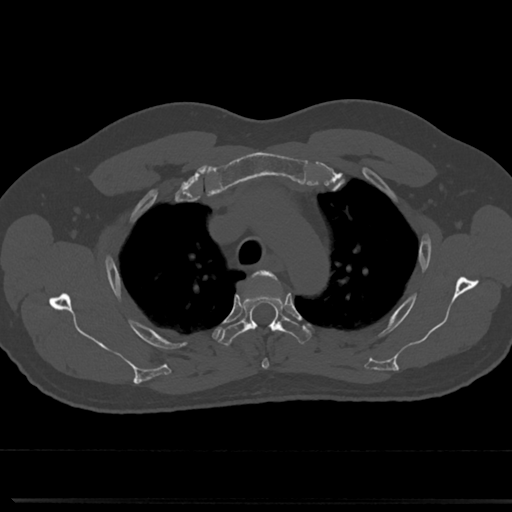
CT including the spine, one axial slice; position 561 of 817 along the scan axis; 120 kVp; bone window (W 1800 / L 400 HU); 512 × 512 image matrix. Male patient, age 61 years. From the clinical record (not read from this slice): primary cancer: prostate.
Structures marked on this image (semi-automatic segmentation, software-assisted and operator-edited):
- T3 vertebra: bounding box <255,271,269,368> (left, top, right, bottom; pixels)
- T4 vertebra: <219,272,311,345>